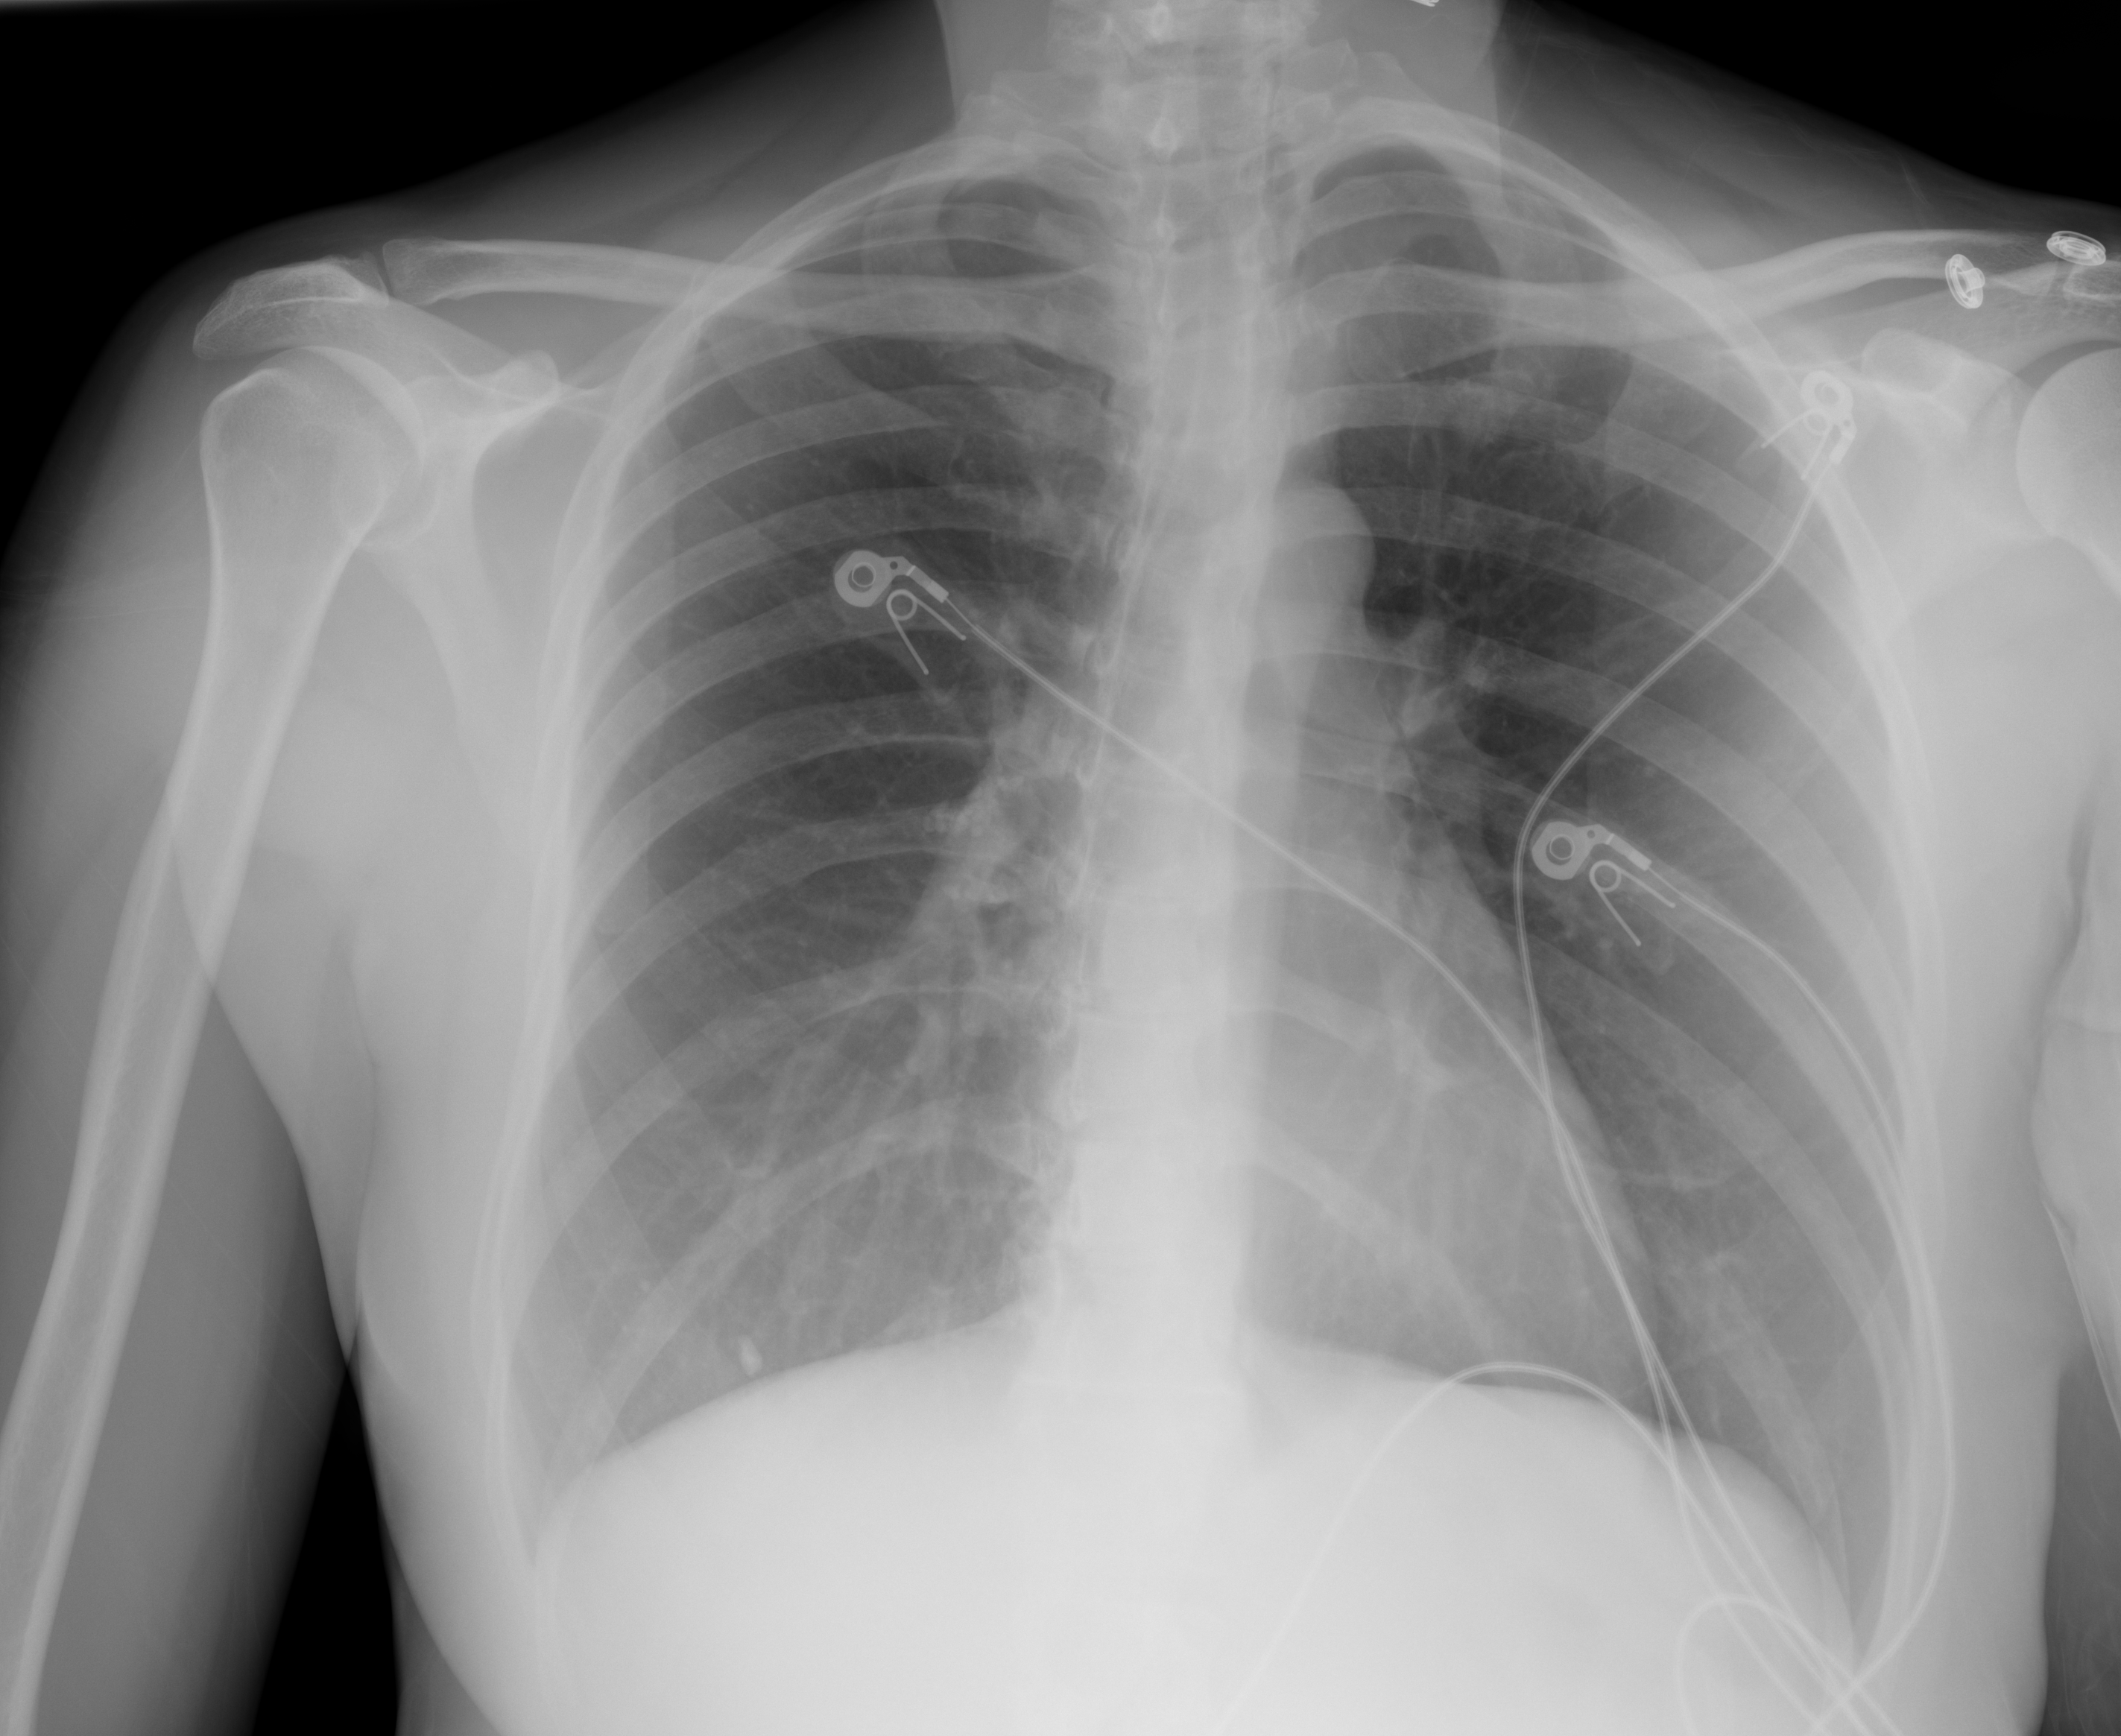
Chest X-ray (portable), AP projection. Female patient, age 48 years; COVID-19 (test-positive).
Radiologist's key findings for this exam: No significant pleural effusions. No acute consolidation.